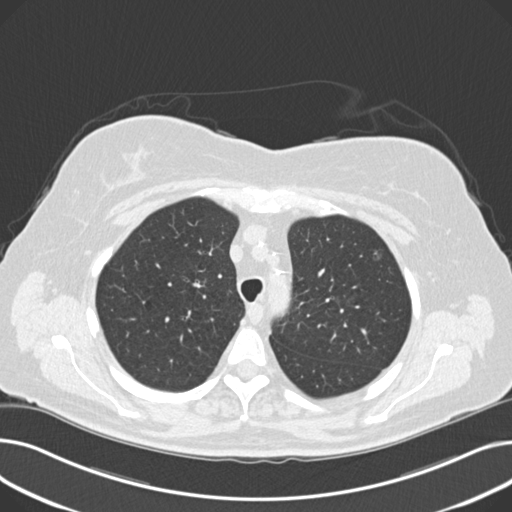
Axial slice from a low-dose chest CT screening exam, third annual screen, lung window (W 1500 / L -600 HU), 2 mm slice thickness, slice 55 of 203 in the series, 512 × 512 image matrix, field of view 372 × 372 mm. Female, age 60 years at enrolment.
Lesion marked by an expert reader, bounding box <359,240,401,278> (left, top, right, bottom; pixels). The screening reader recorded 8 non-calcified nodules or masses ≥4 mm on this exam (right upper lobe, lingula, lingula, right middle lobe, right lower lobe, left lower lobe, left lower lobe, left lower lobe); which of them this box marks is not recorded. Official screen result: positive, other. Participant outcome: lung cancer diagnosed 176 days after this screen — non-small cell carcinoma, left upper lobe, poorly differentiated (G3), stage IB (AJCC 6th edition), 7 mm at pathology.